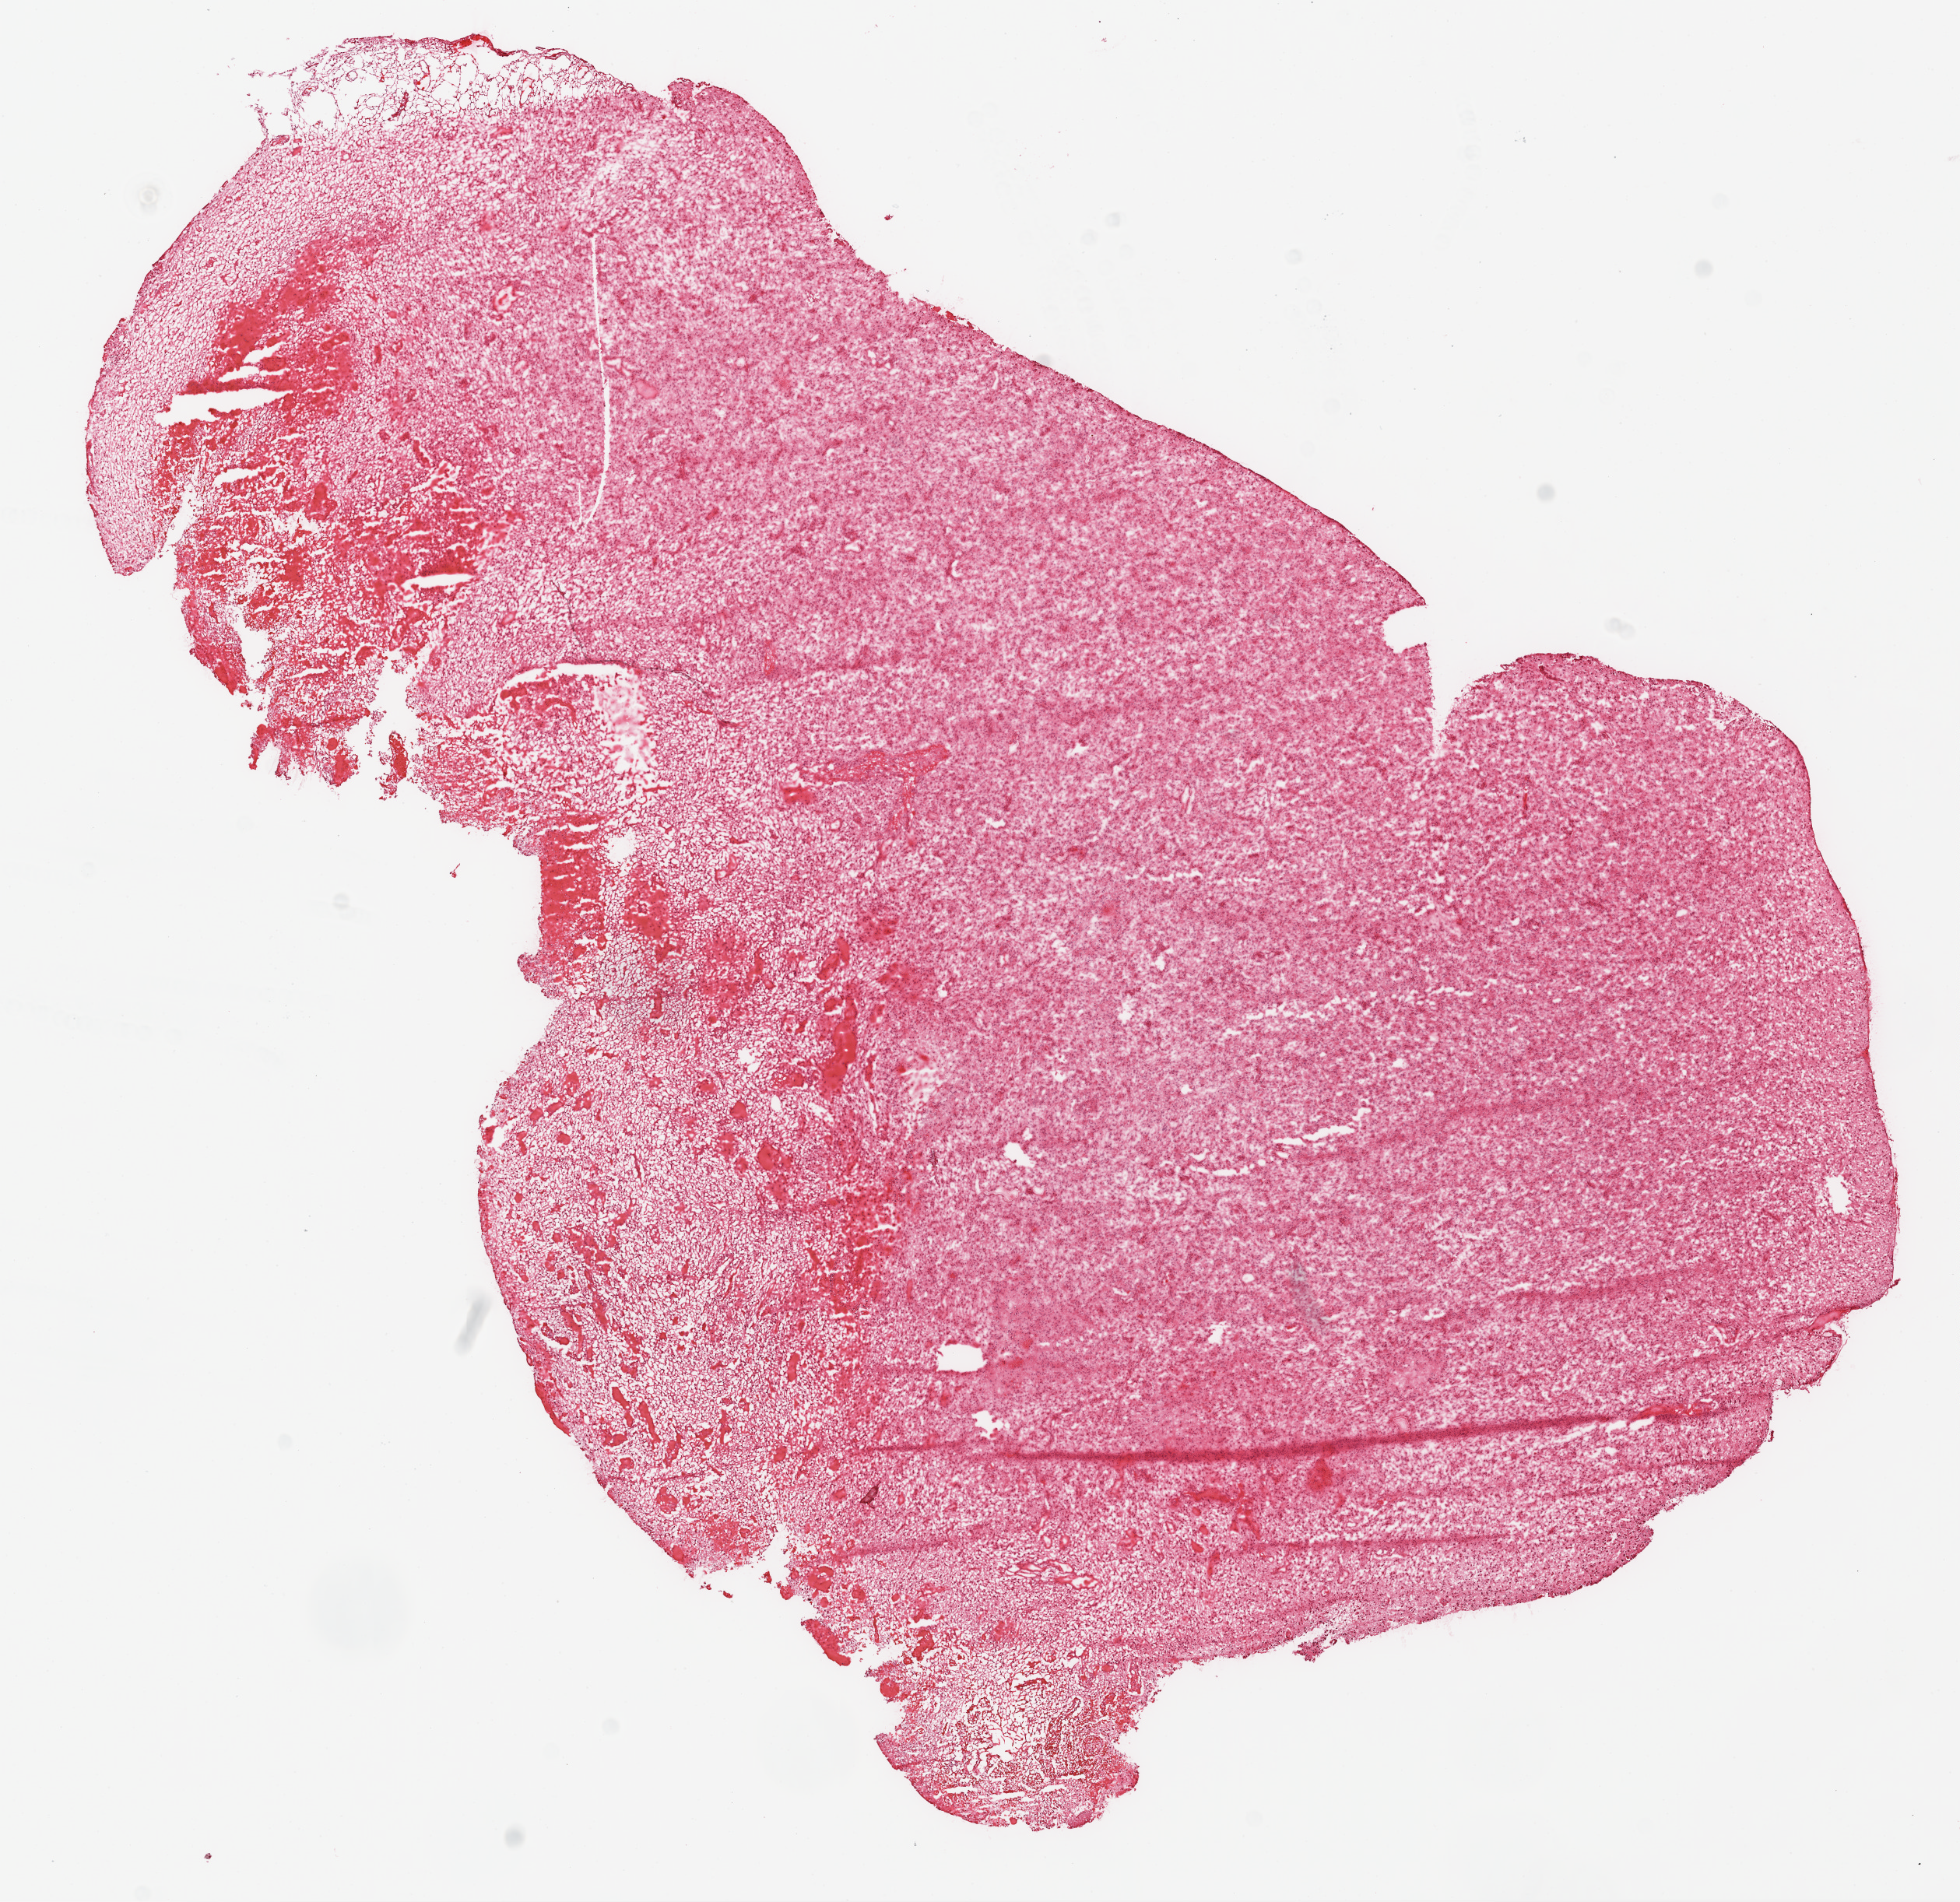
H&E-stained whole-slide image, low-resolution overview of the scanned area, about 10.2 x 9.9 mm. Frozen section from the top of the tissue portion. Sample: primary tumour, brain. Male, age 53 years at initial diagnosis. Pathologist review of this section (percent, as recorded): tumour cells 100%, tumour nuclei 100%, normal cells 0%, stromal cells 0%, necrosis 0%.
- pathologic diagnosis: Glioblastoma